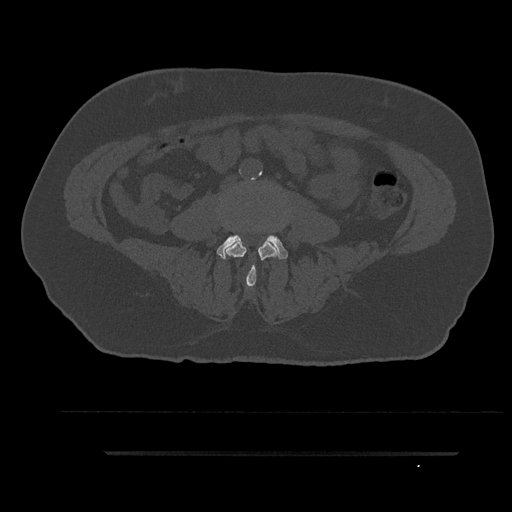
CT including the spine, one axial slice. Position 6 of 797 along the scan axis. Bone window (W 1800 / L 400 HU). 0.5 mm slice thickness. 512 × 512 image matrix. Male patient, age 63 years. Case-level facts recorded for this patient, not image findings: primary cancer: renal; vertebrae with lytic lesions (as recorded): T8.
Structures marked on this image (semi-automatic segmentation, software-assisted and operator-edited):
- L3 vertebra: bounding box <225,239,277,286> (left, top, right, bottom; pixels)
- L4 vertebra: <216,235,288,279>